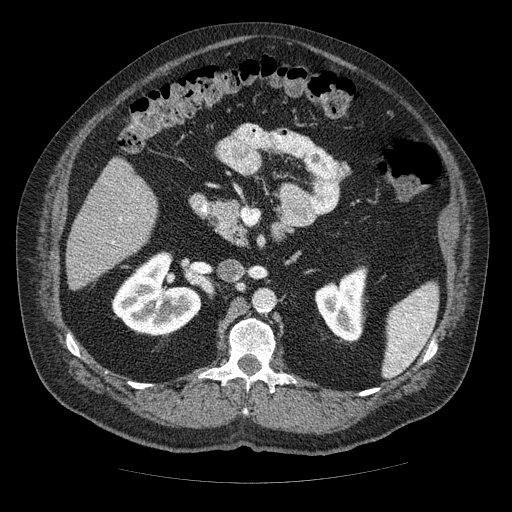
Contrast-enhanced abdominal CT (liver protocol), one axial slice; slice 19 of 85 in the series (ordered by position); reconstruction kernel STANDARD; soft-tissue window (W 400 / L 40 HU); 2.5 mm slice thickness; 512 × 512 image matrix, field of view 420 × 420 mm. Case-level facts recorded for this patient, not image findings: diagnosis: hepatocellular carcinoma (patient treated with transarterial chemoembolisation; whether this scan precedes or follows treatment is not stated here); TNM stage (as recorded): Stage-IIIA; Child-Pugh class: A; tumour nodularity: multinodular; tumour size: 7 cm.
Structures marked on this image (semi-automatic segmentation, software-assisted and operator-edited):
- liver parenchyma outside the tumour (the mass and vessels are separate outlines, so this box may not span the whole liver): bounding box [x1, y1, x2, y2] px = [66, 158, 156, 288]
- liver vessels: [112, 217, 122, 244]